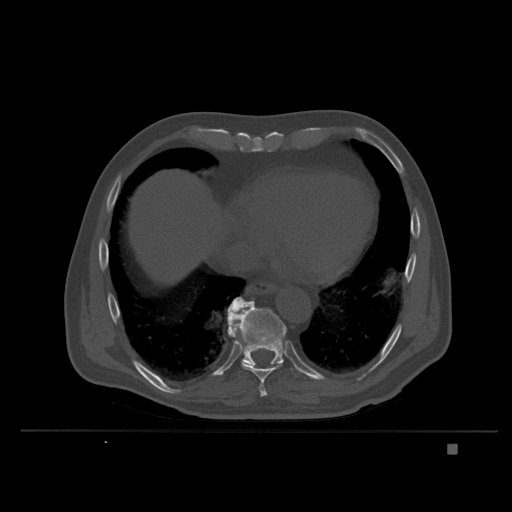
CT including the spine, one axial slice. Slice 205 of 435 in the series (ordered by position). Bone window (W 1800 / L 400 HU). 1.5 mm slice thickness. 512 × 512 image matrix, field of view 434 × 434 mm. Patient: male, 73 years. From the clinical record (not read from this slice): primary cancer: skin.
Structures marked on this image (semi-automatic segmentation, software-assisted and operator-edited):
- T10 vertebra: bounding box <236,305,287,366> (left, top, right, bottom; pixels)
- T9 vertebra: <228,297,284,397>